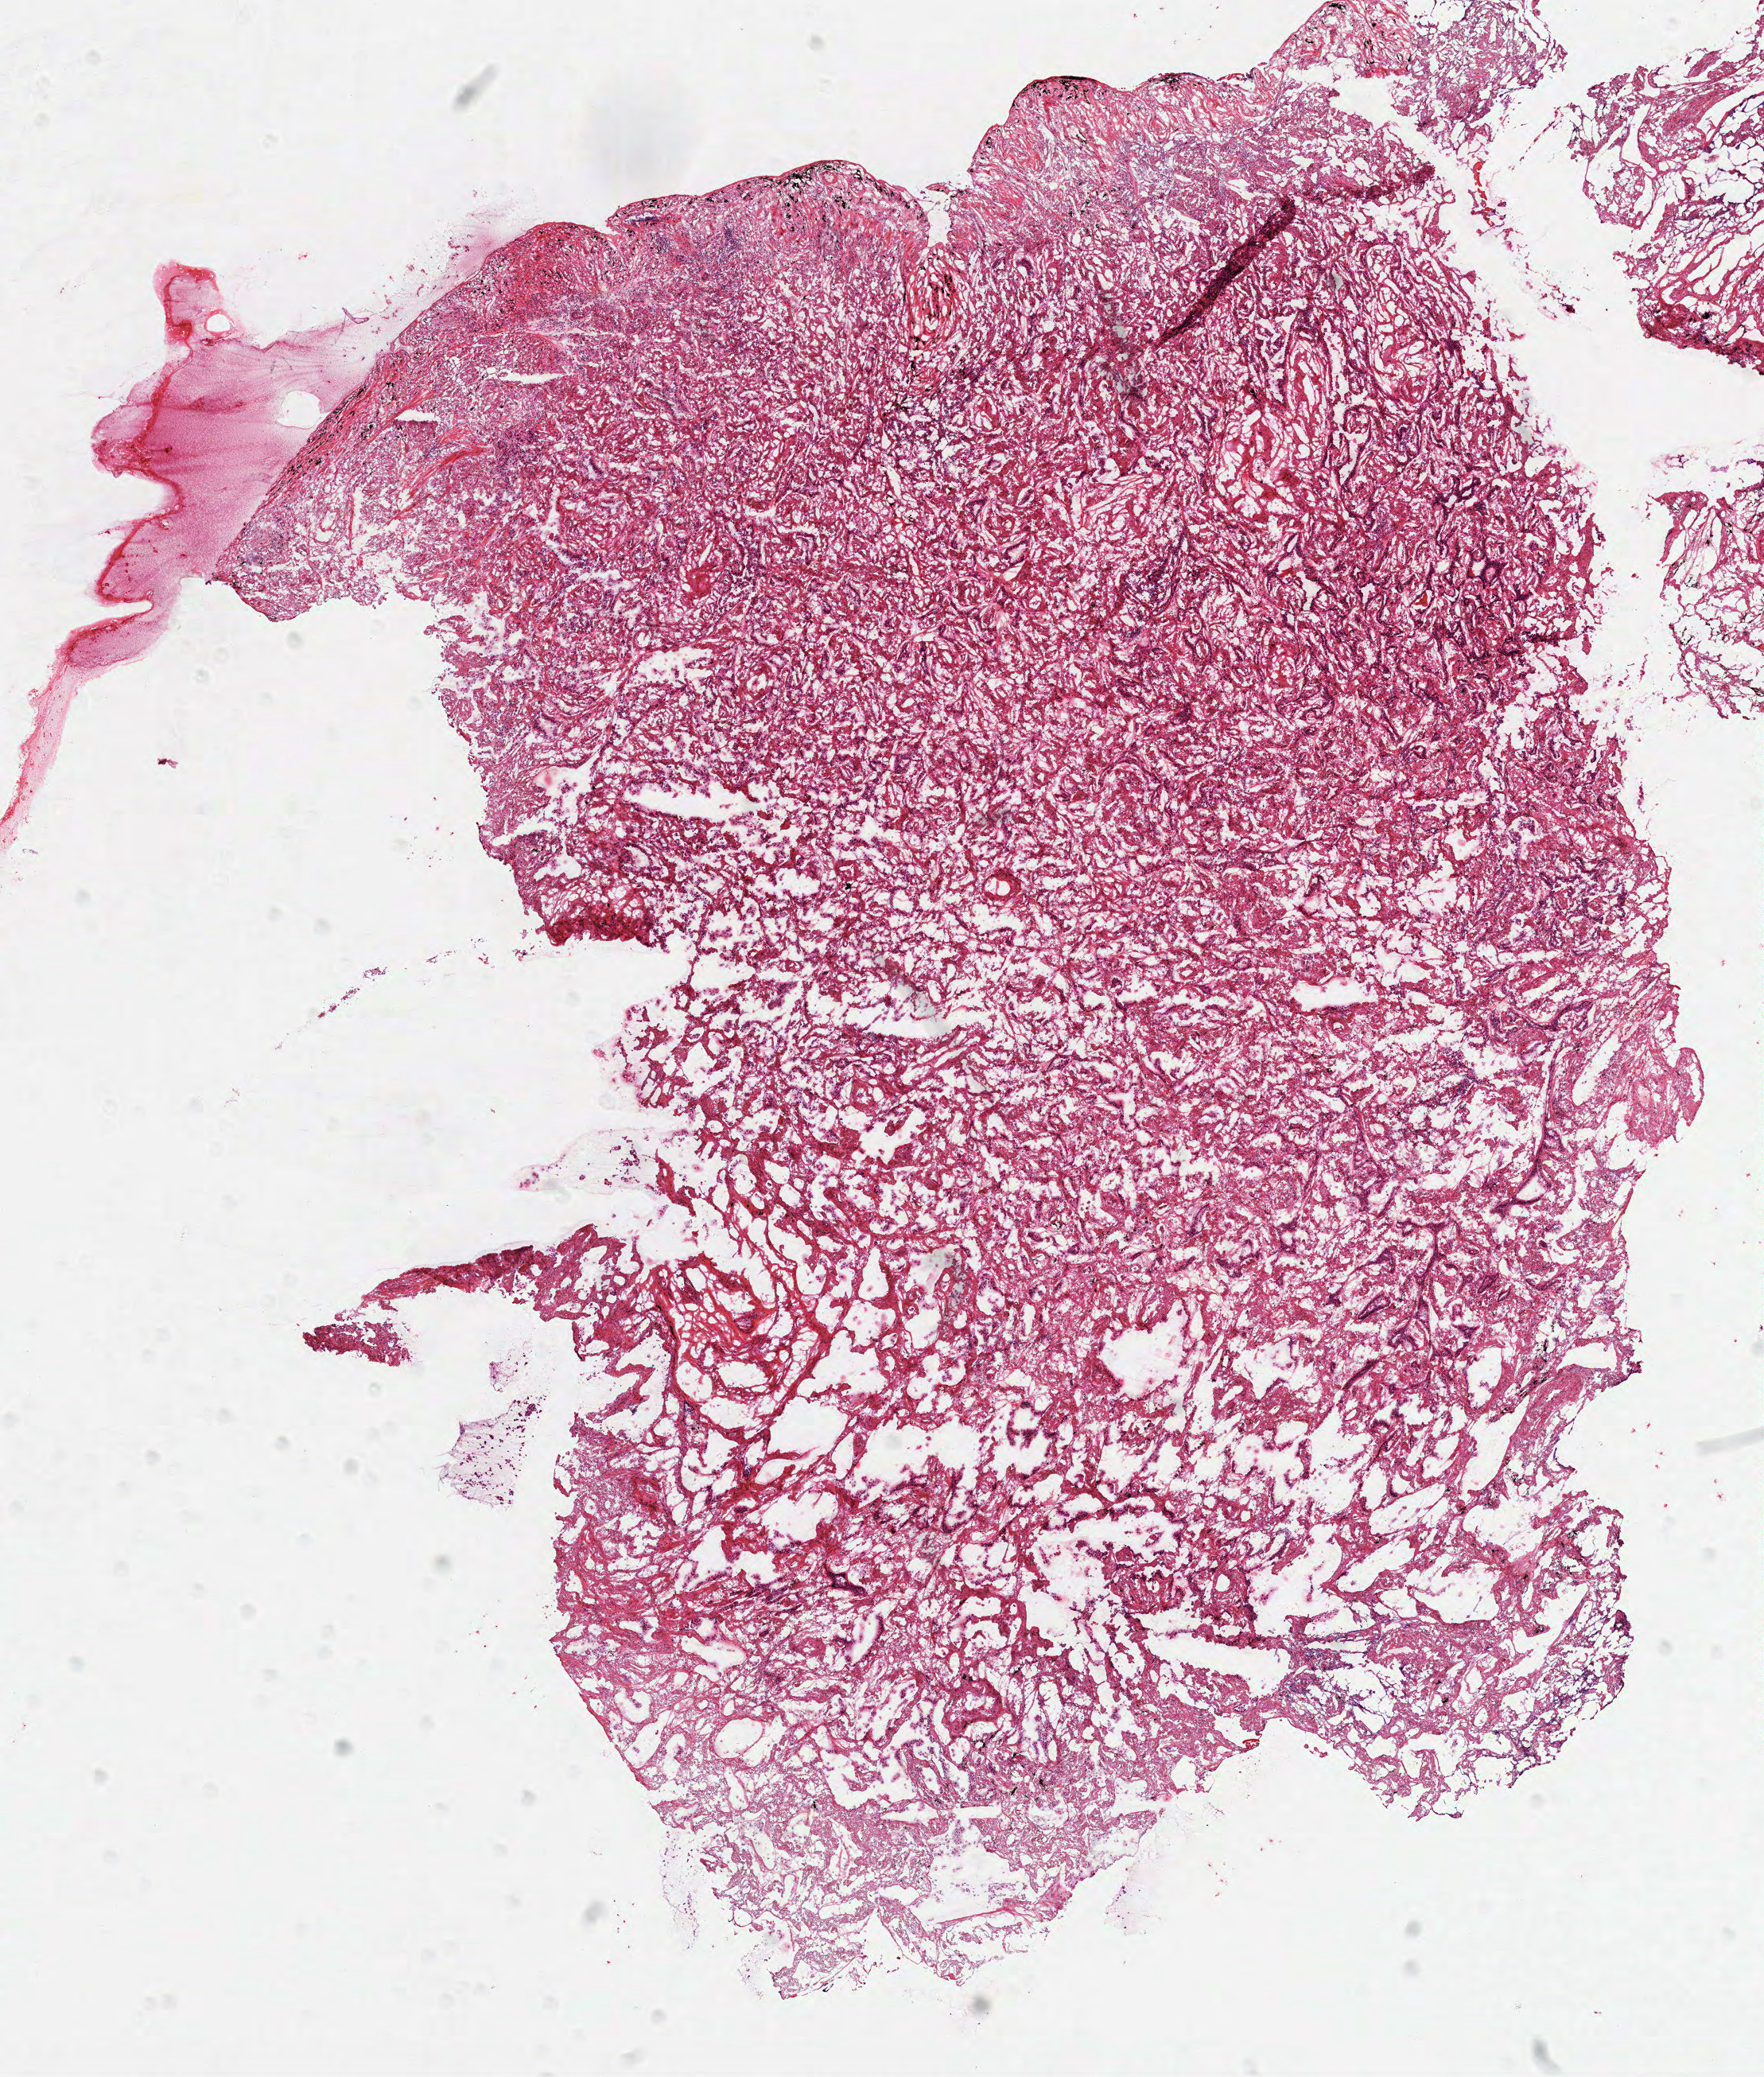
Digitized H&E tissue section (whole slide), low-resolution overview of the scanned area, about 8.9 x 10.5 mm. Frozen section. Lung, primary tumour sample. Female patient; age at initial diagnosis 63 years. Pathologist review of this section (percent, as recorded): tumour cells 65%, tumour nuclei 60%, normal cells 15%, stromal cells 20%, necrosis 0%.
AJCC pathologic stage: IA (7th edition). Laterality: right. Diagnosis: Adenocarcinoma with mixed subtypes.